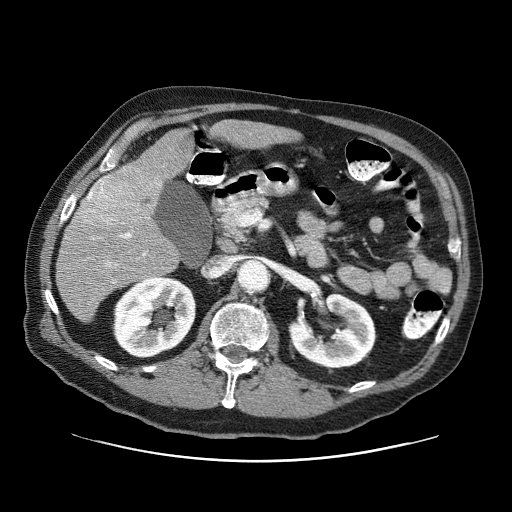
Contrast-enhanced abdominal CT (liver protocol), one axial slice; slice 30 of 87 in the series (ordered by position); one of 3 acquisitions stored at this slice position; soft-tissue window (W 400 / L 40 HU); 2.5 mm slice thickness; 512 × 512 image matrix, field of view 400 × 400 mm. Case-level facts recorded for this patient, not image findings: diagnosis: hepatocellular carcinoma (patient treated with transarterial chemoembolisation; whether this scan precedes or follows treatment is not stated here); TNM stage (as recorded): Stage-IIIA; Child-Pugh class: A; tumour differentiation: well differentiated.
Annotated regions visible in this slice (semi-automatic segmentation, software-assisted and operator-edited):
- liver parenchyma outside the tumour (the mass and vessels are separate outlines, so this box may not span the whole liver): bounding box [x1, y1, x2, y2] px = [56, 120, 300, 322]
- mass: [72, 164, 161, 230]
- liver vessels: [93, 233, 146, 283]